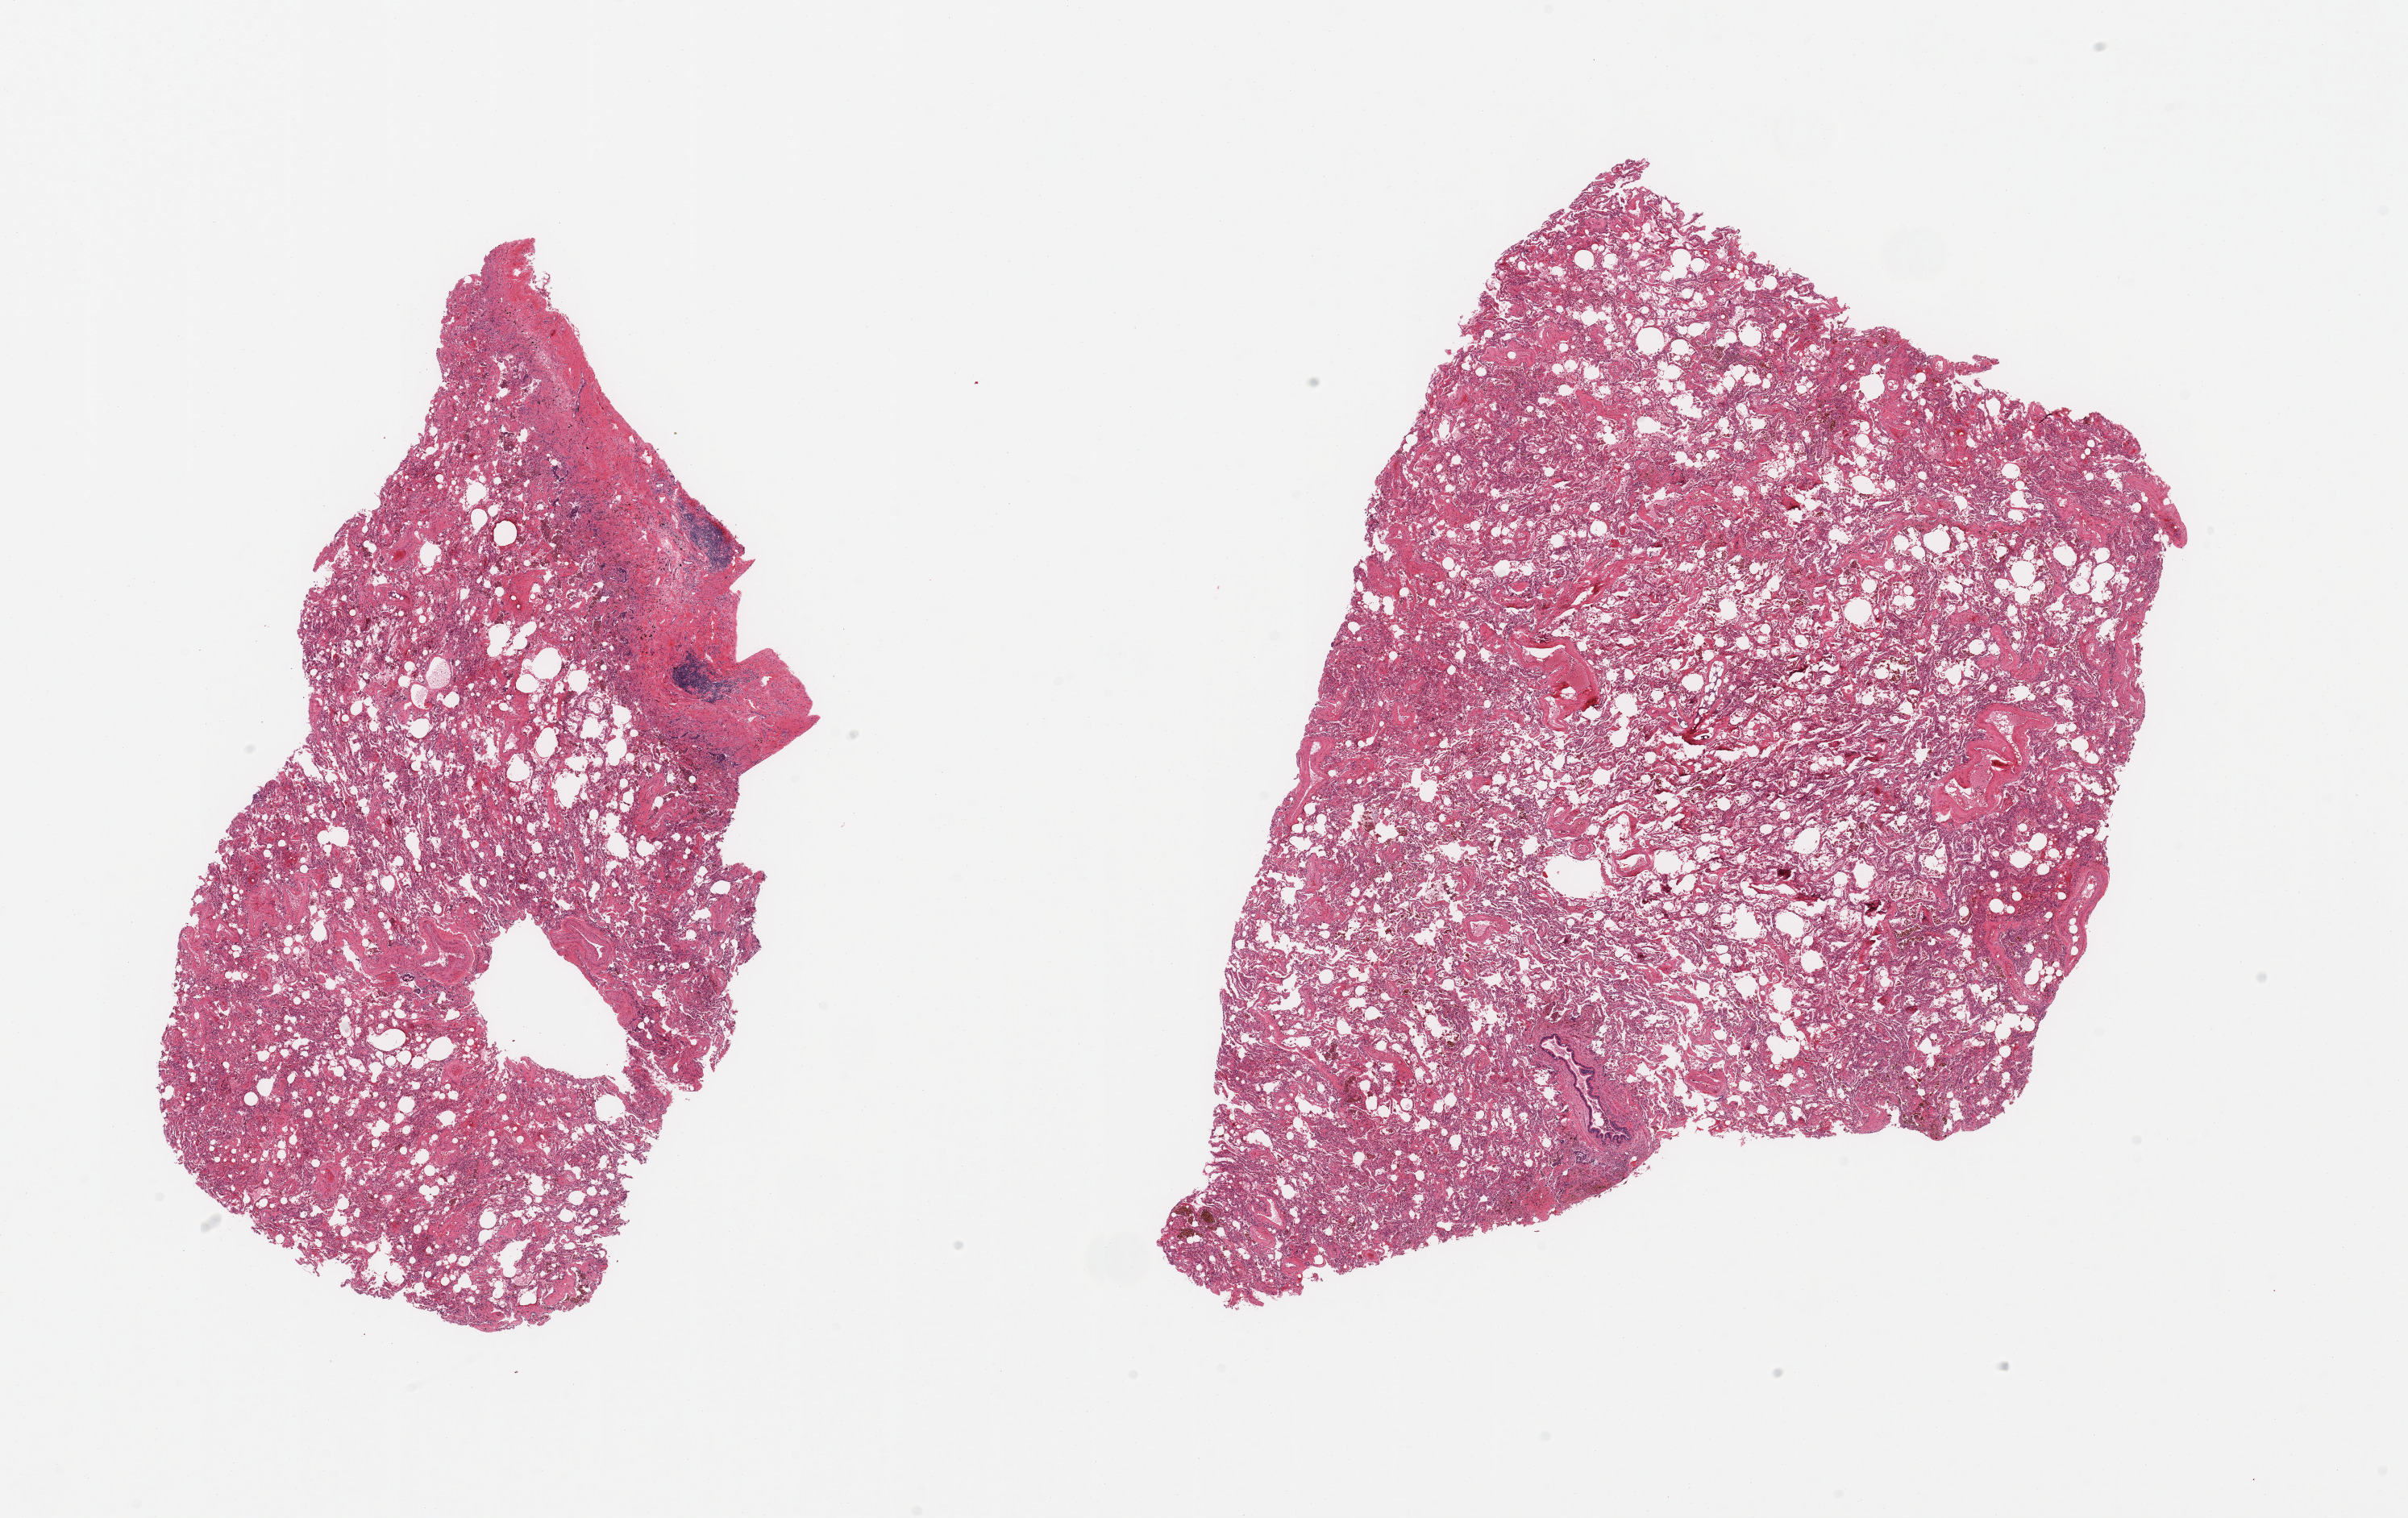
Digitized H&E-stained section, low-resolution overview of the scanned area, about 23.6 x 14.9 mm; PAXgene-fixed, paraffin-embedded tissue; section of lung (target tissue); donor tissue sample.
* reviewer comment on this tissue sample: 2 pieces, chronic interstitial pneumonitis with fibrosis and hyaline membrane formation, chronic injury pattern